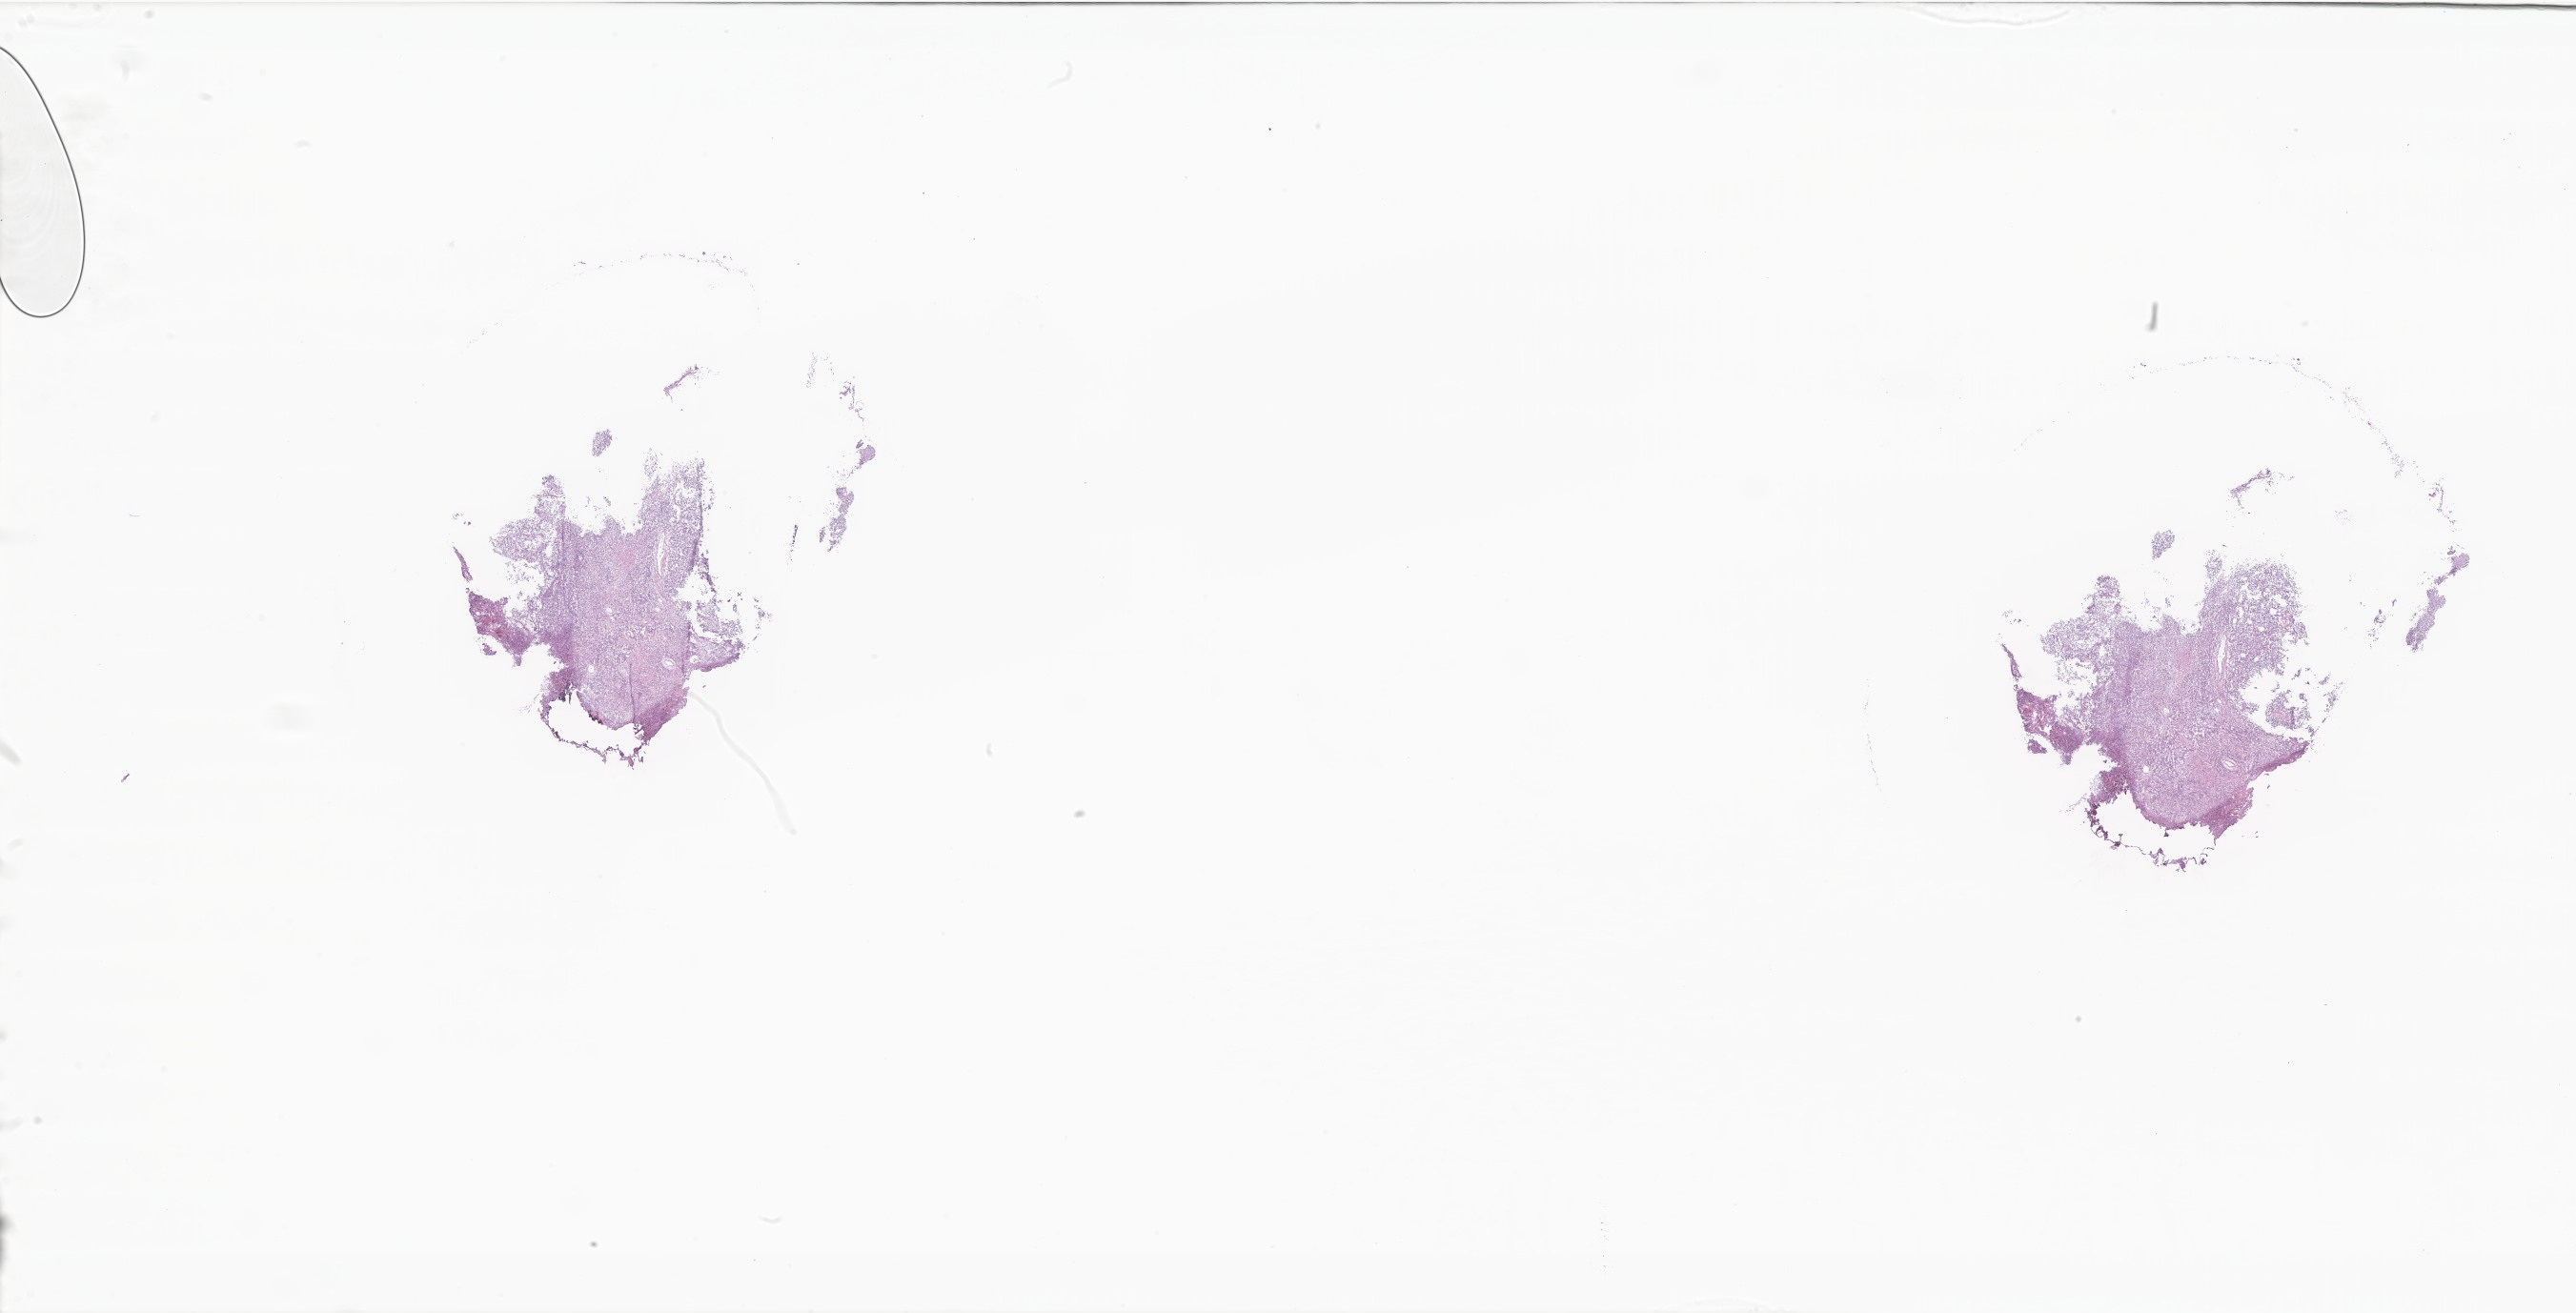
Digitized hematoxylin and eosin (H&E)-stained section of tumor tissue from the brain — low-resolution overview of the scanned area, about 45.6 x 23.2 mm; frozen section. Patient: female, age 86 months (7 years 2 months).
Diagnosis: Astroblastoma.